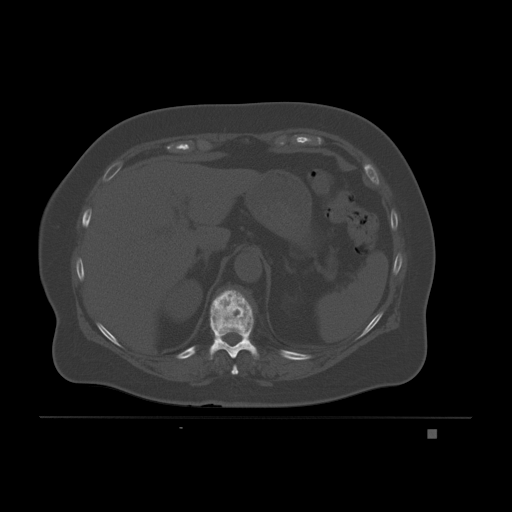
CT including the spine, one axial slice. Slice 99 of 221 in the series (ordered by position). Bone window (W 1800 / L 400 HU). 3 mm slice thickness. 512 × 512 image matrix, field of view 474 × 474 mm. Patient: female, 63 years. Case-level facts recorded for this patient, not image findings: primary cancer: breast.
Annotated regions visible in this slice (semi-automatic segmentation, software-assisted and operator-edited):
- T10 vertebra: box from (x=209, y=289) to (x=260, y=360) px
- T9 vertebra: (x=231, y=364)–(x=238, y=375)